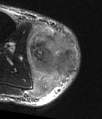
MRI of an extremity soft-tissue mass, one axial slice. Position 19 of 48 along the scan axis. T2-weighted fat-saturated. MR volume resampled by the dataset authors to the PET/CT grid (not the native acquisition matrix). 3.27 mm slice thickness. 102 × 119 image matrix, field of view 100 × 116 mm. Male patient. Case-level facts recorded for this patient, not image findings: histological type: pleiomorphic liposarcoma; grade: high; site of the primary tumour: right calf.
Structures marked on this image (expert contour drawn on MRI and transferred to this co-registered scan by the dataset authors):
- gross tumour volume including surrounding oedema: box from (x=28, y=26) to (x=75, y=98) px
- gross tumour volume (mass): (x=30, y=32)–(x=75, y=75)